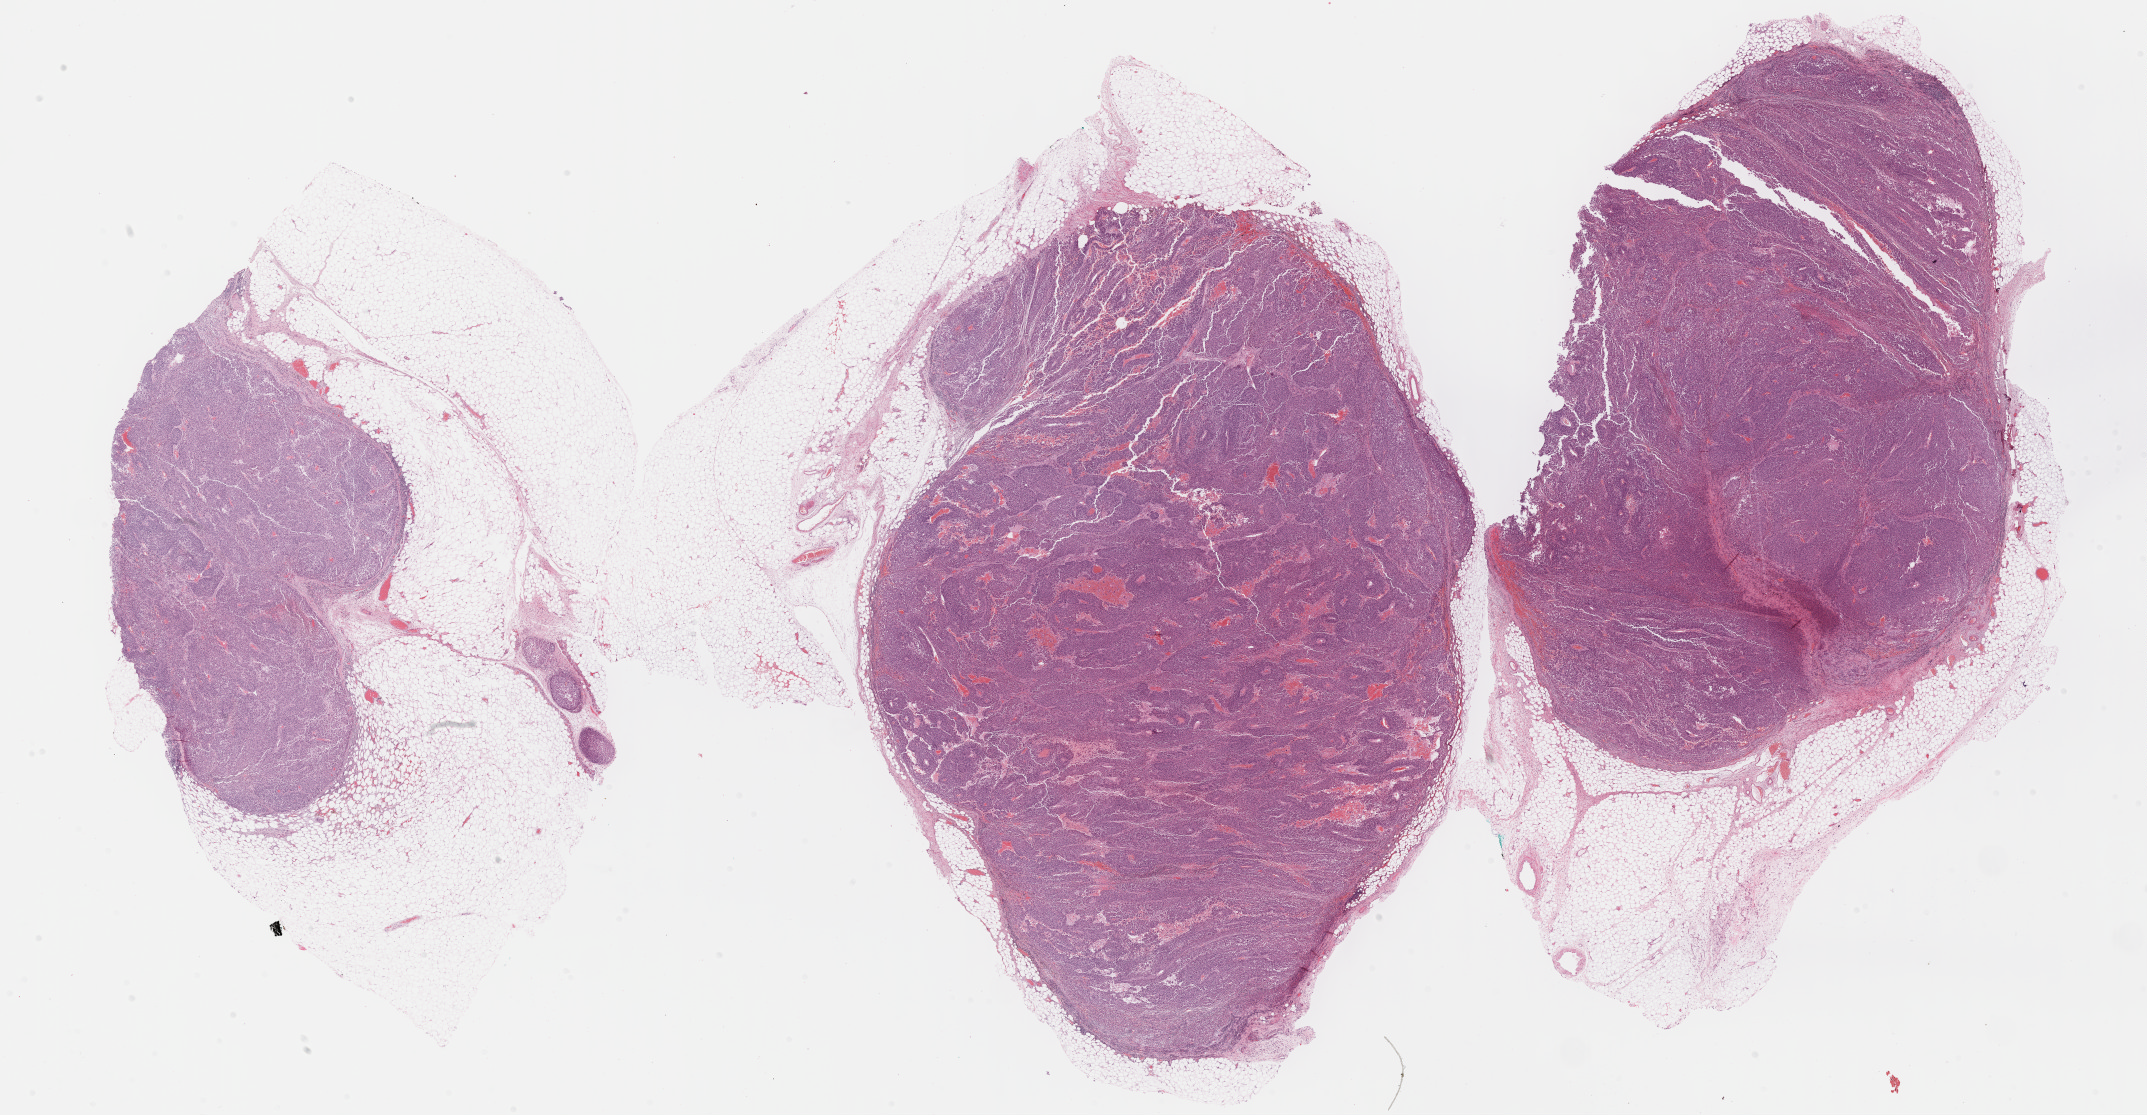
H&E whole-slide image — whole scanned area (about 34.7 x 18.0 mm) shown as a low-resolution overview. Formalin-fixed paraffin-embedded (FFPE) diagnostic section. Metastatic tumour sample, sampled site: lymph nodes of inguinal region or leg. Patient: female, age at initial diagnosis 84 years.
This section: metastatic tumour tissue. Patient diagnosis: Malignant melanoma, NOS.